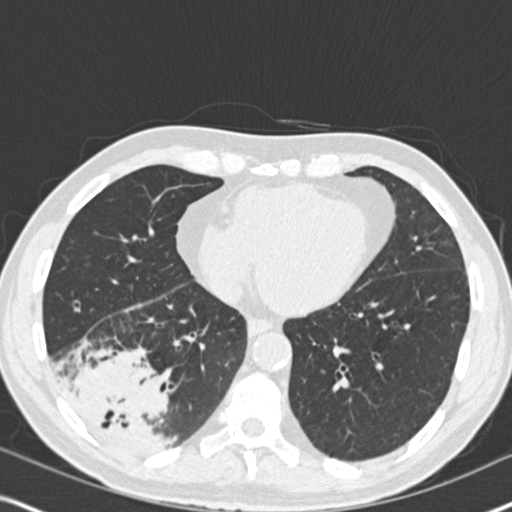
Chest CT (low-dose screening protocol), one axial image; second screening round (one year after baseline); lung window (W 1500 / L -600 HU); 2 mm slice thickness; standard (soft-tissue) reconstruction kernel (B30f); 120 kVp; 512 × 512 image matrix. Male participant, aged 61 years at enrolment. Current smoker at enrolment.
Lesion marked by an expert reader, bounding box <46,320,188,463> (left, top, right, bottom; pixels). The exam's reader record, not a measurement of the box and not confirmed to be the same lesion: non-calcified nodule or mass ≥4 mm, right lower lobe, 90 × 80 mm, soft tissue attenuation, pre-existing on the prior screen: yes; interval growth: yes.